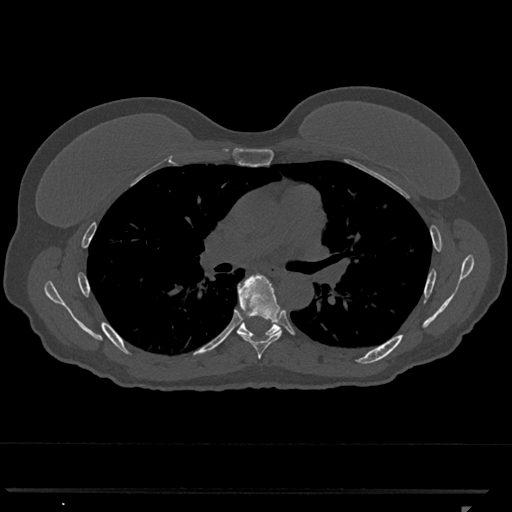
CT including the spine, one axial slice. Position 743 of 793 along the scan axis. Reconstruction kernel Br40s/3. Bone window (W 1800 / L 400 HU). 512 × 512 image matrix, field of view 380 × 380 mm. Female patient, age 62 years. From the clinical record (not read from this slice): primary cancer: renal.
Outlined on this slice (semi-automatically segmented with operator editing):
- T6 vertebra: bounding box (x1, y1, x2, y2) in pixels: (237, 273, 282, 359)
- T7 vertebra: (236, 318, 280, 338)